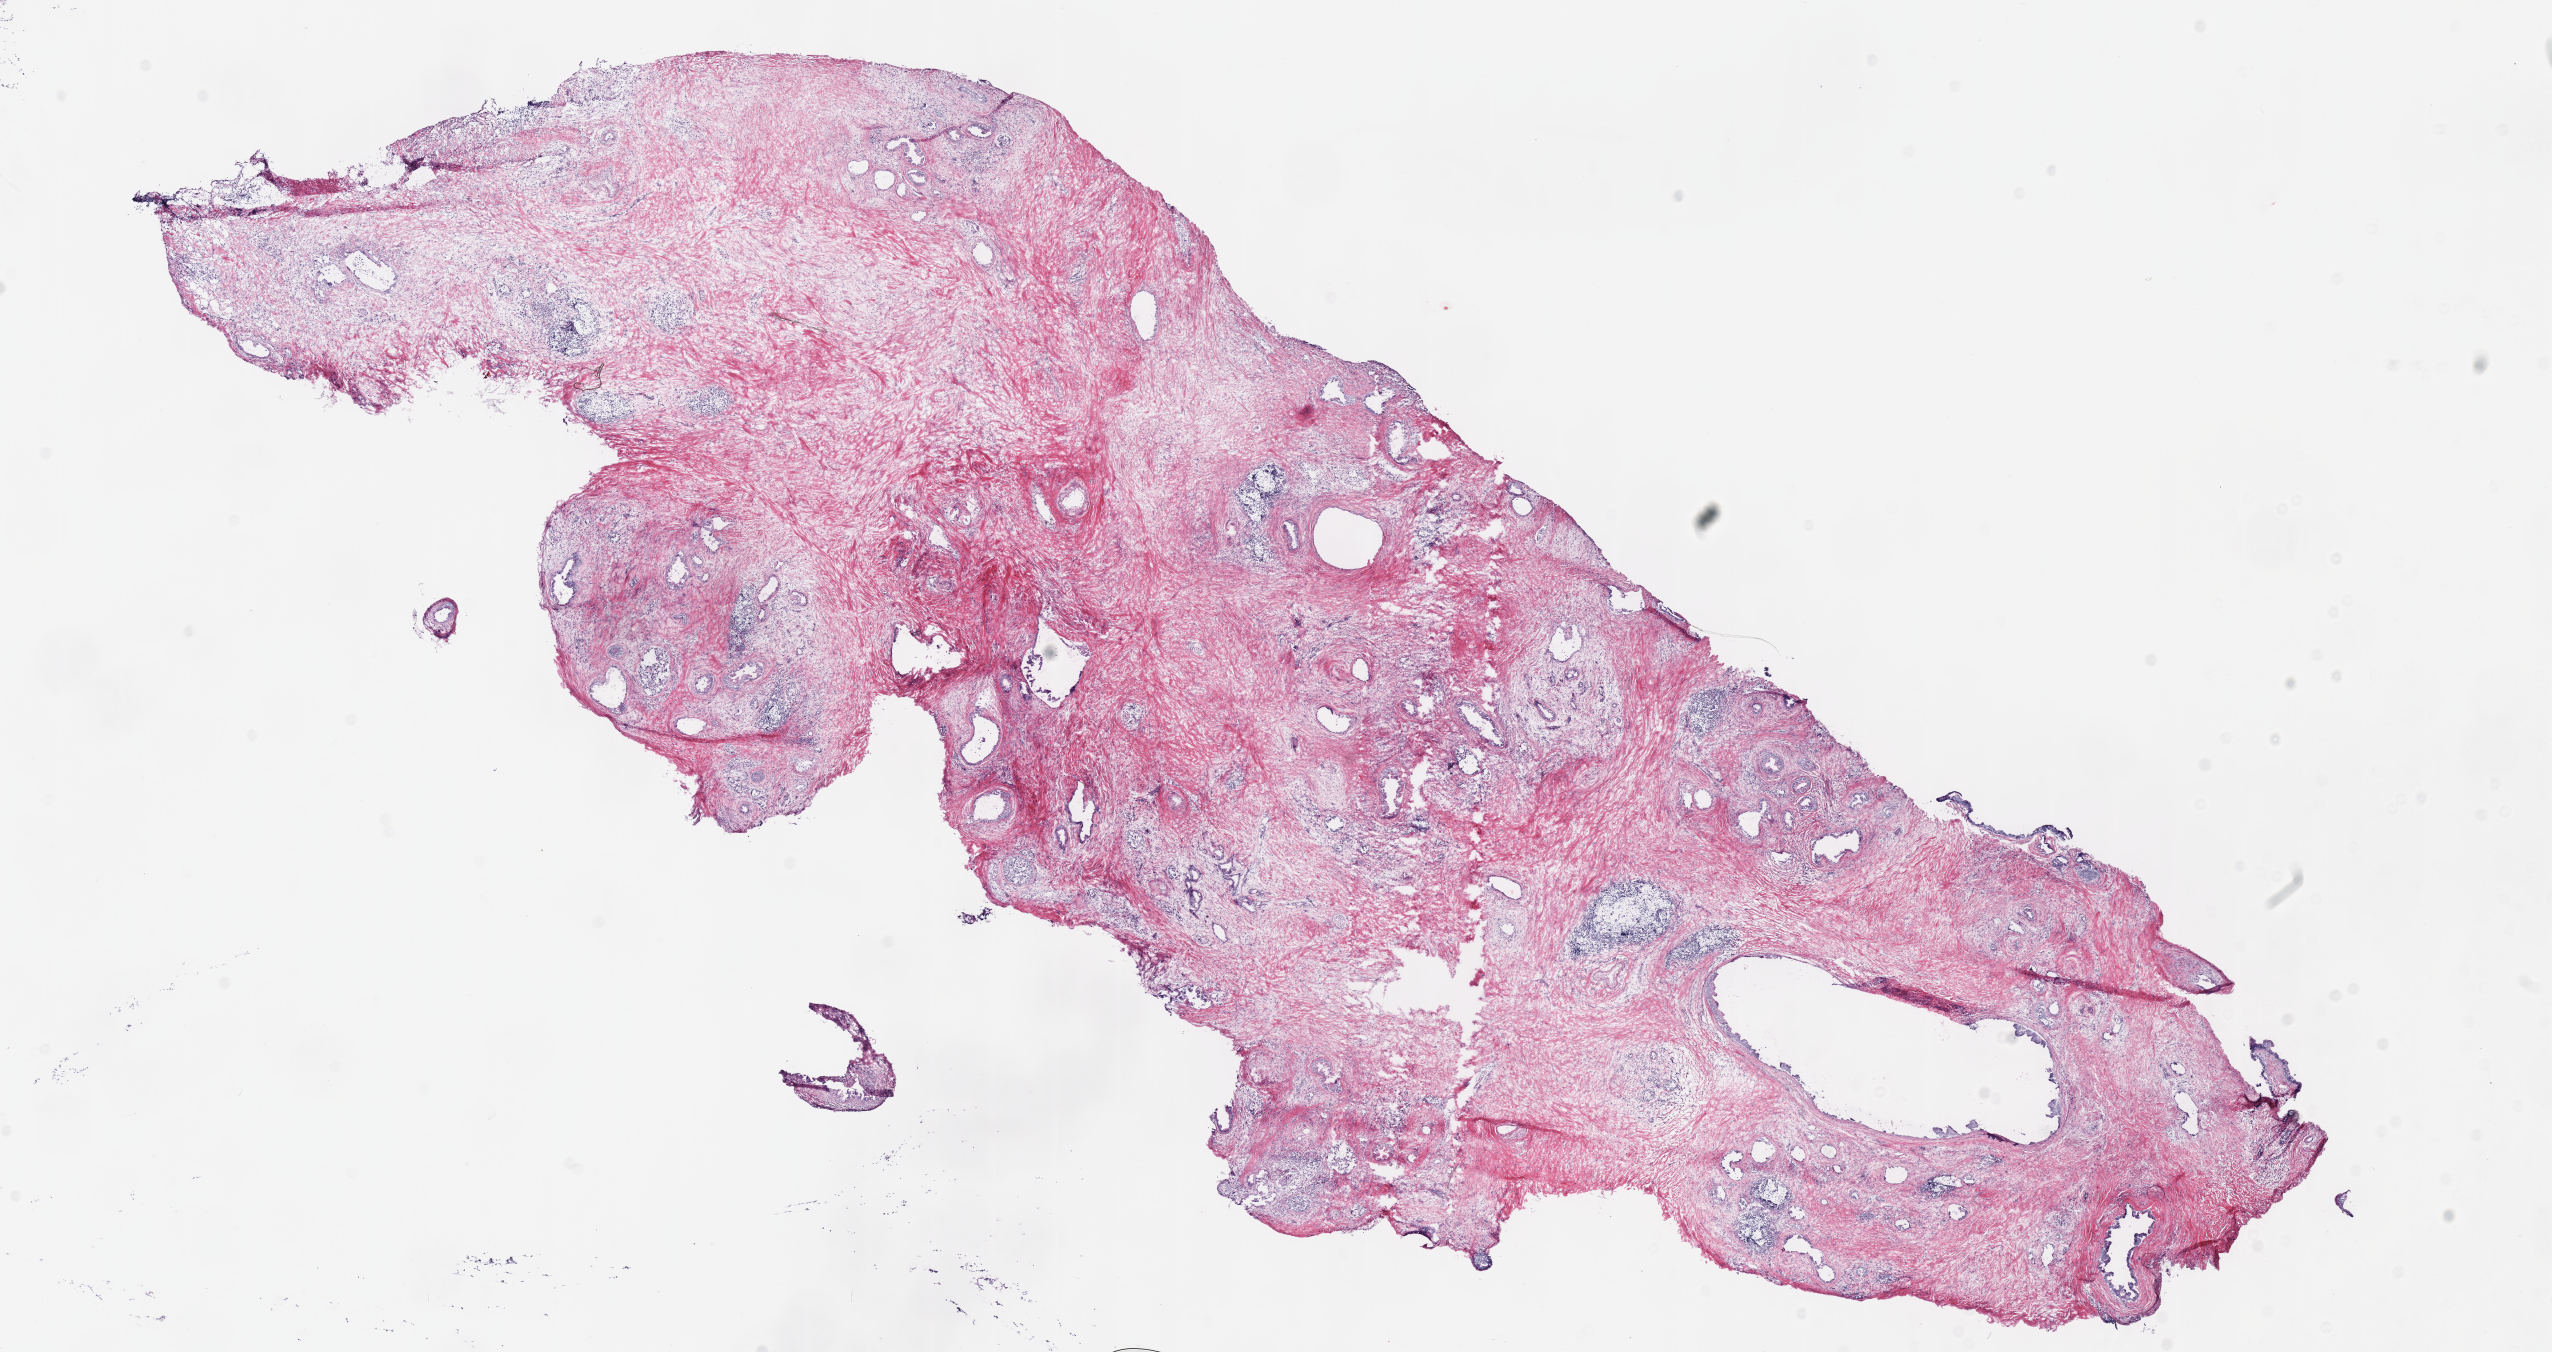
Digitized H&E-stained tissue section (whole slide) — low-resolution overview of the scanned area, about 20.1 x 10.6 mm (acquisition: 40x scan), frozen section from the top of the tissue portion, sample: primary tumour, pancreas. Patient: female, age at initial diagnosis 66 years. Histologic grade: G2 (moderately differentiated). Pathologist review of this section (percent, as recorded): tumour cells 60%, tumour nuclei 60%, normal cells 0%, stromal cells 40%, necrosis 0%.
Lymph nodes positive (case pathology): 0 of 12 examined. Pathologic diagnosis: Infiltrating duct carcinoma, NOS. AJCC pathologic stage: IIA (6th edition).